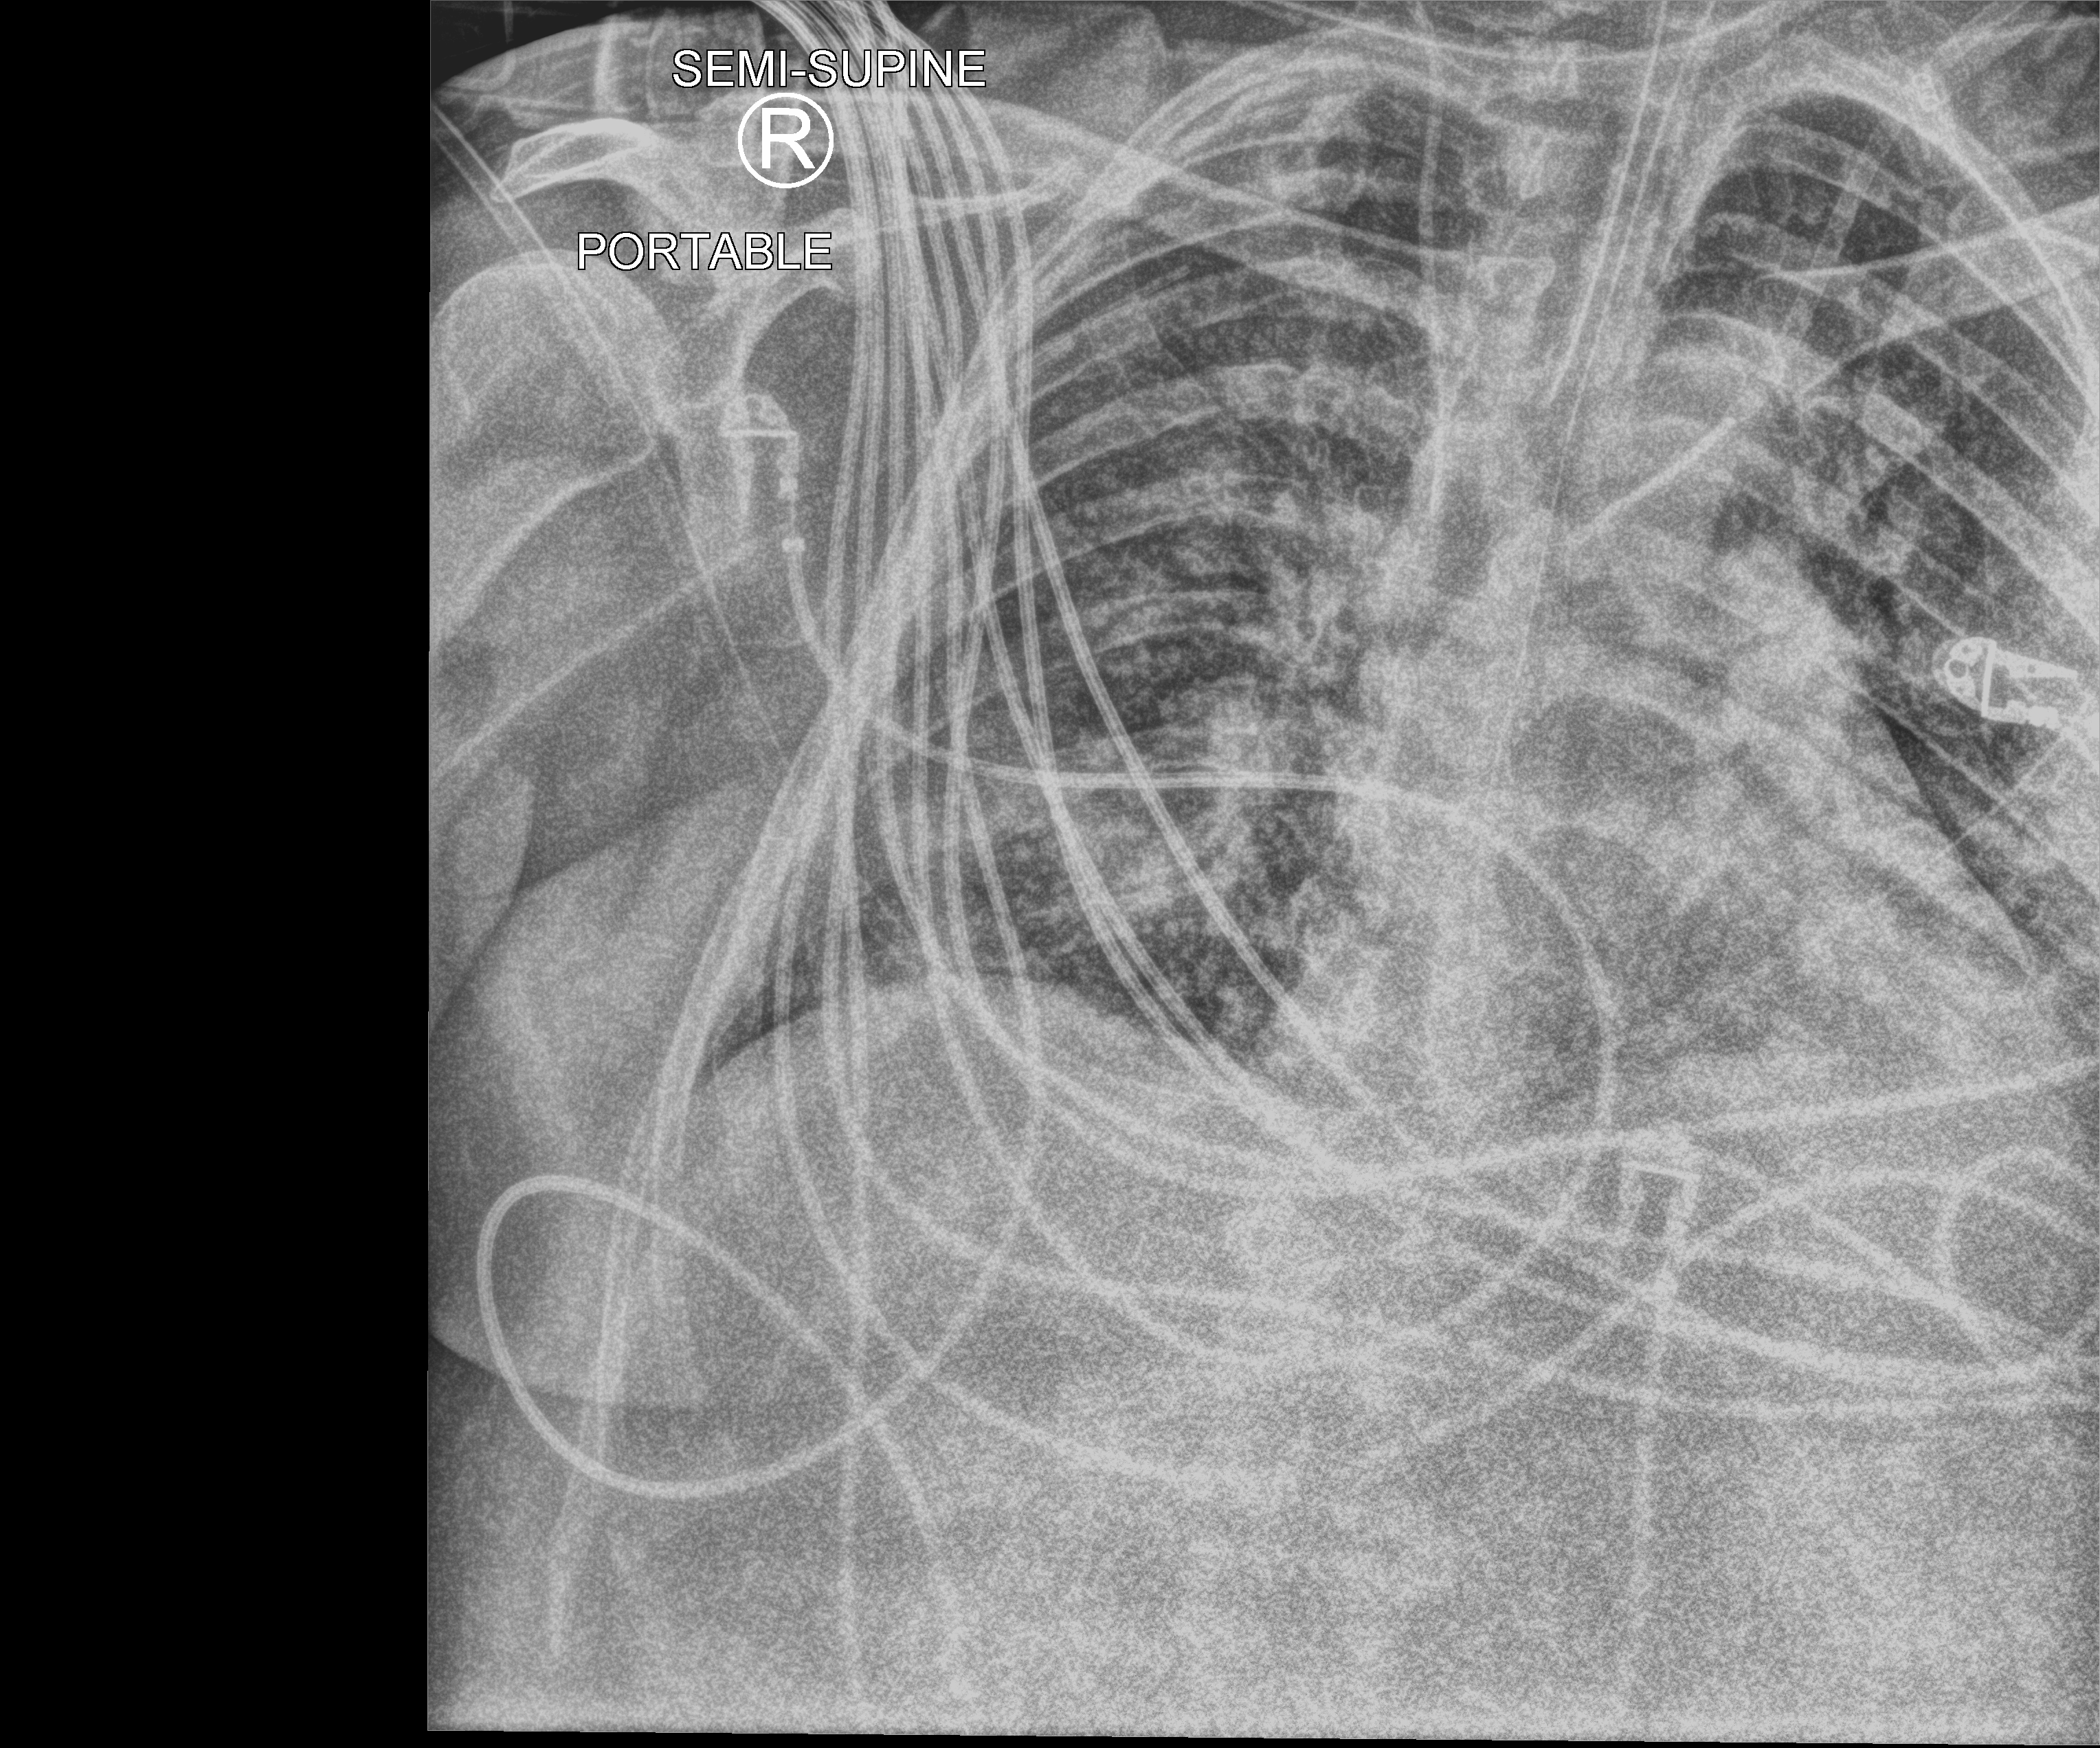
Chest X-ray (portable); anteroposterior (AP) projection. Patient hospitalised with COVID-19; male, aged 18–59 years.
From the hospital-stay record, not from the radiograph (when in the stay this image was taken is not recorded): other chronic lung disease (admission record): no; mechanically ventilated during this hospital stay: yes; admitted to intensive care during this hospital stay: yes.